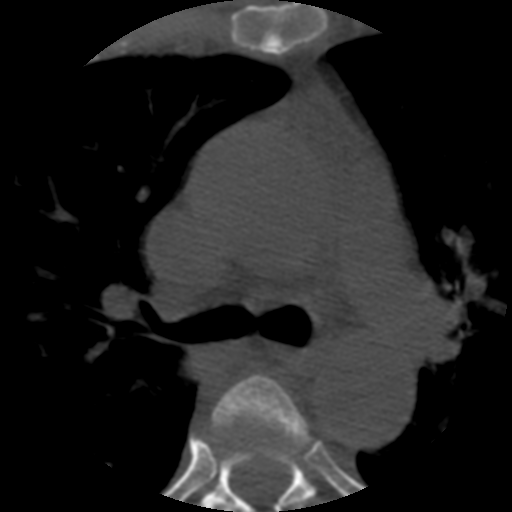
CT including the spine, one axial slice; slice 384 of 508 in the series (ordered by position); reconstruction kernel STANDARD; 120 kVp; bone window (W 1800 / L 400 HU); 1.25 mm slice thickness; 512 × 512 image matrix, field of view 160 × 160 mm. Patient age 57 years. Case-level facts recorded for this patient, not image findings: primary cancer: prostate.
Structures marked on this image (semi-automatic segmentation, software-assisted and operator-edited):
- T4 vertebra: bounding box <211,374,310,453> (left, top, right, bottom; pixels)
- T5 vertebra: <199,377,318,512>